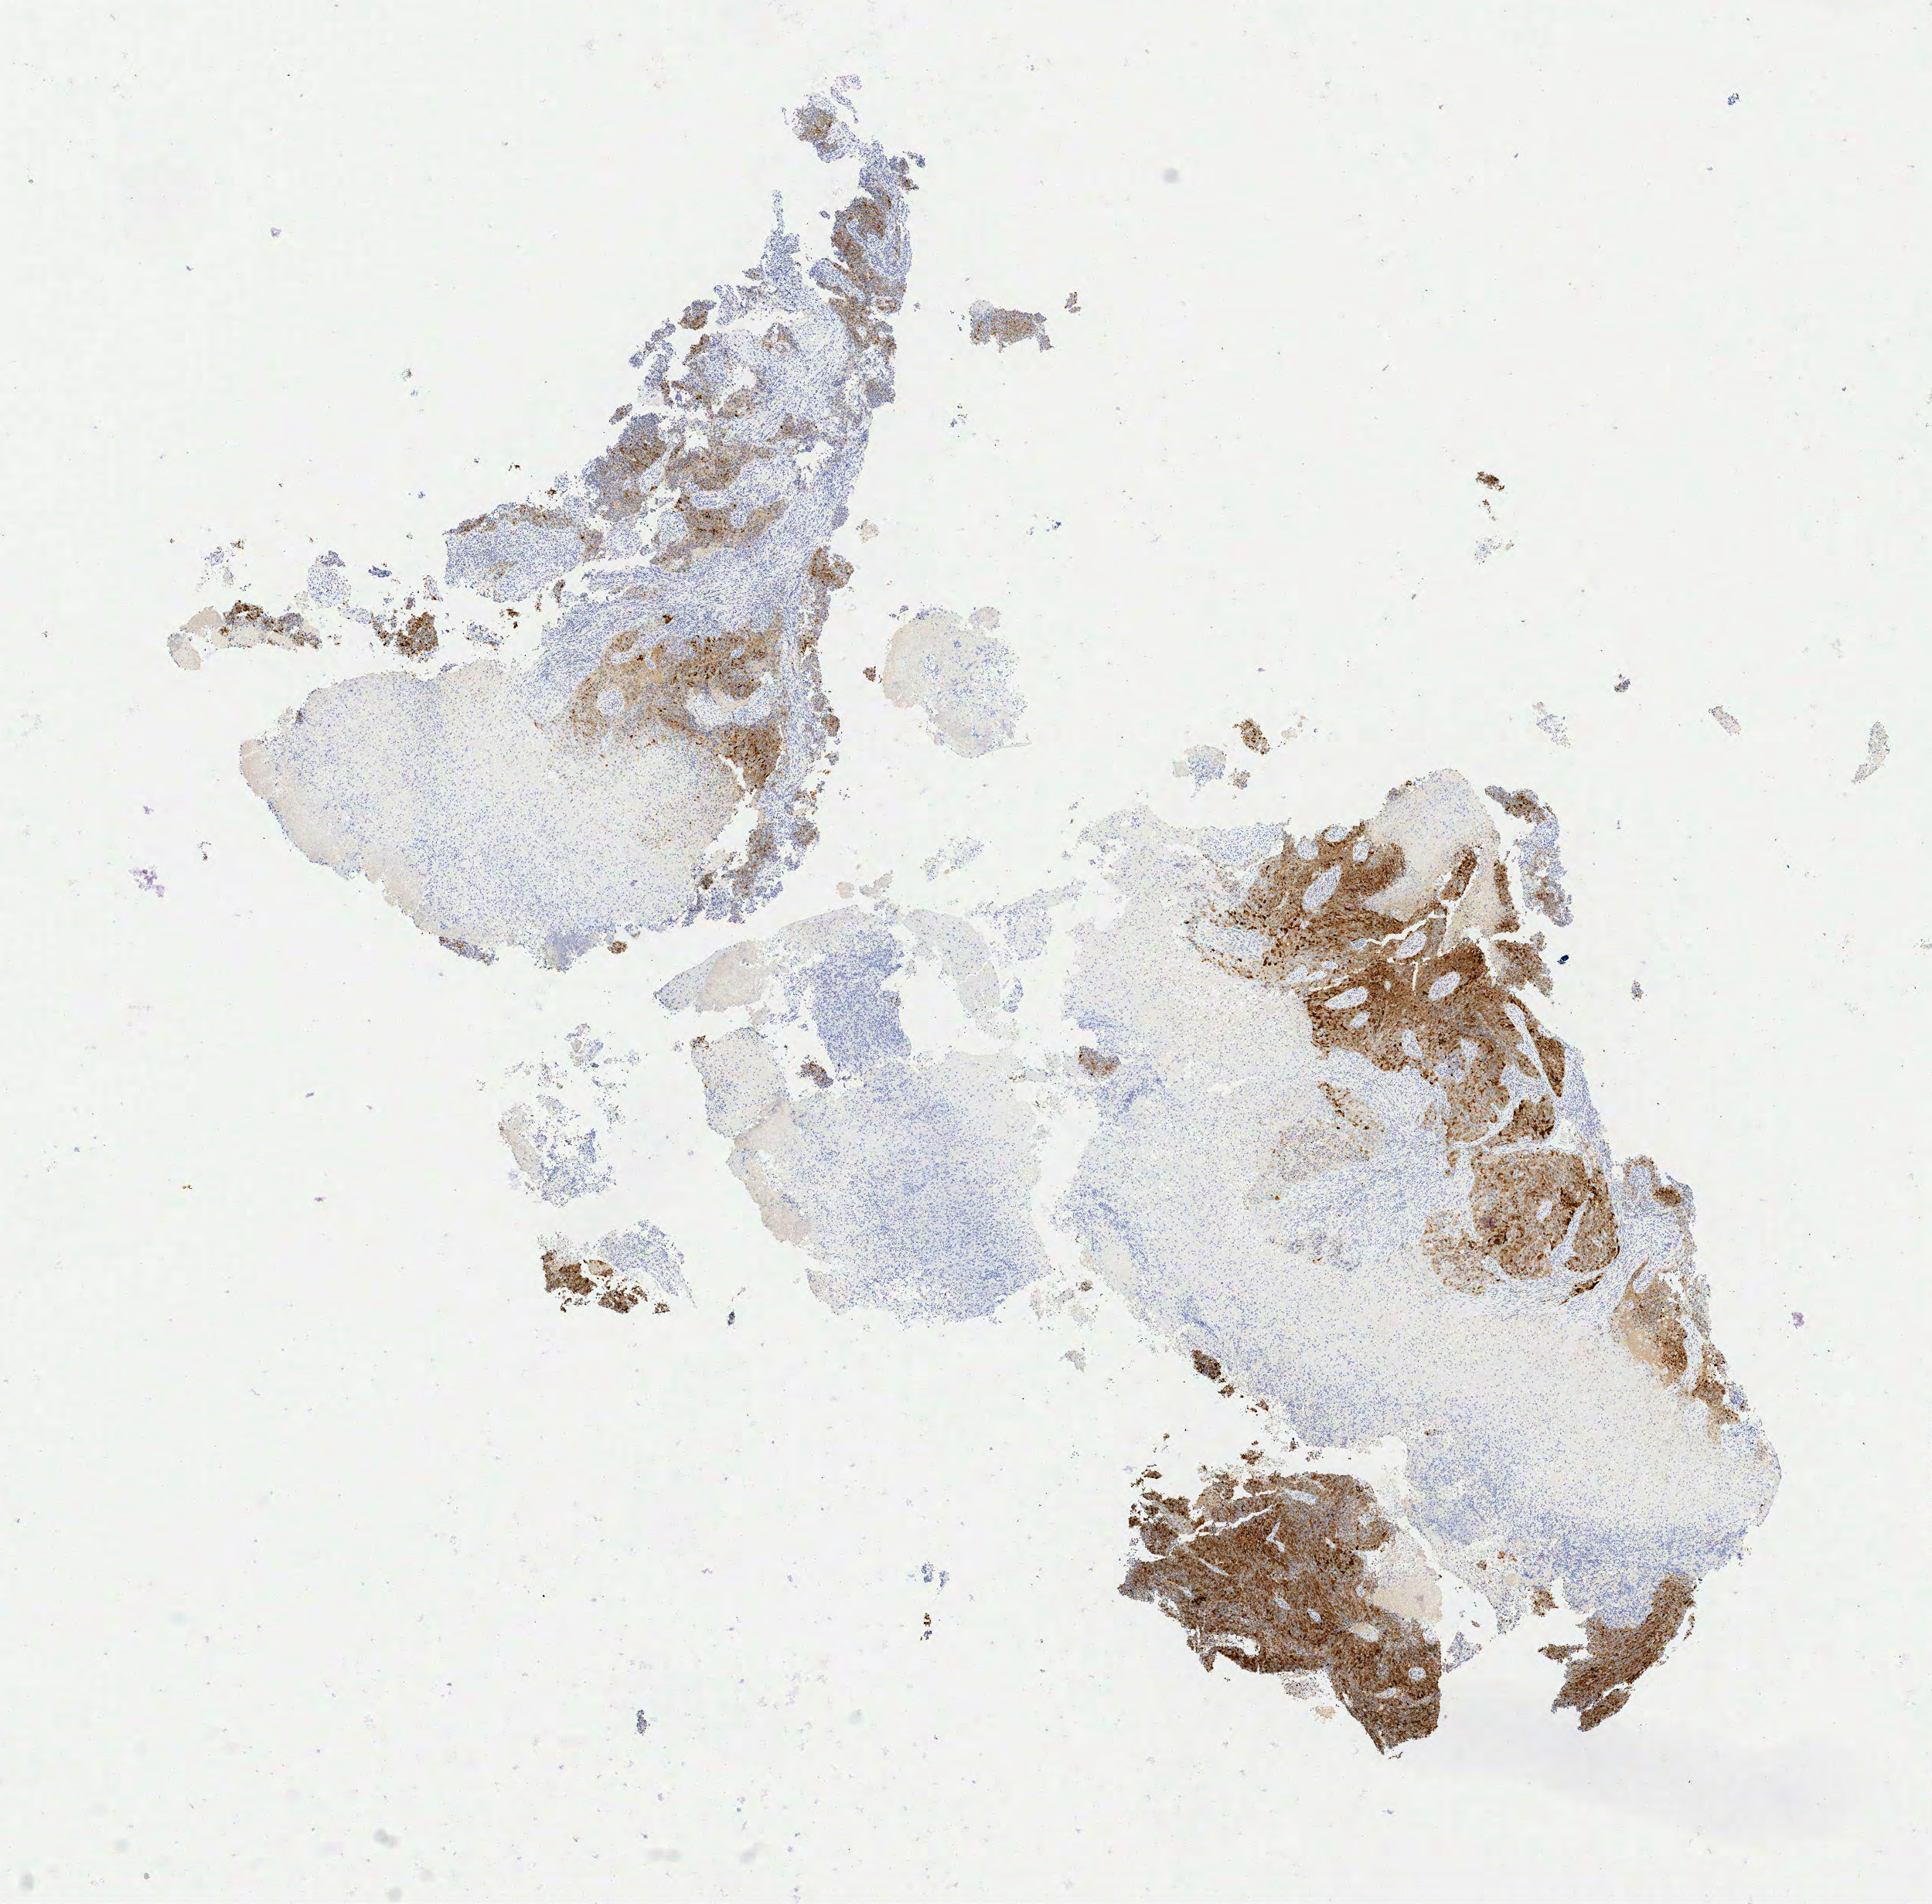
Whole-slide image, immunohistochemical stain for p16 (p16INK4a), shown as a low-resolution overview of the whole scanned area (about 9.9 x 9.8 mm), tumor tissue, site: cervix. Patient: female, aged 65.
* histologic diagnosis: Squamous cell carcinoma, large cell, nonkeratinizing, NOS